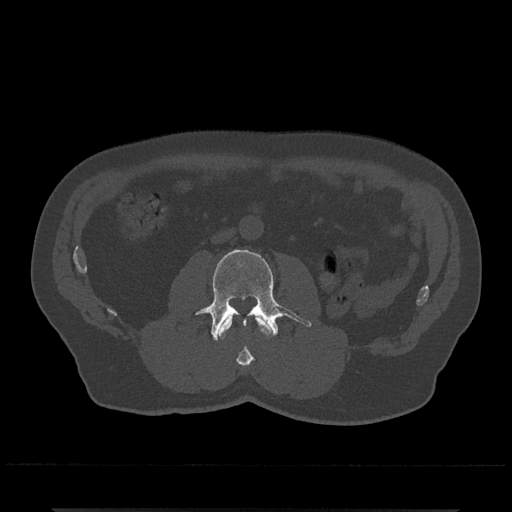
CT including the spine, one axial slice. Slice 238 of 797 in the series (ordered by position). 120 kVp. Bone window (W 1800 / L 400 HU). 0.5 mm slice thickness. 512 × 512 image matrix. Male patient, age 67 years. From the clinical record (not read from this slice): primary cancer: prostate.
Outlined on this slice (semi-automatically segmented with operator editing):
- L2 vertebra: box from (x=218, y=315) to (x=271, y=367) px
- L3 vertebra: (x=197, y=249)–(x=312, y=341)